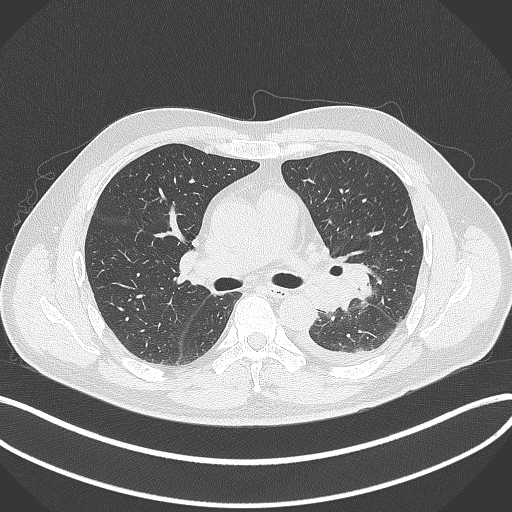
Chest CT, one axial slice; slice 215 of 342 in the series (ordered by position); 120 kVp; lung window (W 1500 / L -600 HU); 1 mm slice thickness; 512 × 512 image matrix. Patient: male, 58 years. Case-level facts recorded for this patient, not image findings: clinical TNM (as recorded): T3 N1 M1b; histopathological grade: G3.
Annotated regions visible in this slice (rectangle marked by the reading radiologist):
- lung tumour (recorded histology: small cell carcinoma): bounding box [x1, y1, x2, y2] px = [337, 259, 379, 303]